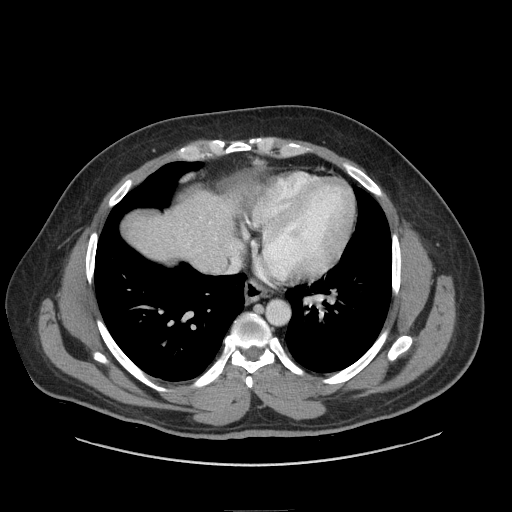
Contrast-enhanced abdominal CT (liver protocol), one axial slice; position 77 of 87 along the scan axis; 140 kVp; soft-tissue window (W 400 / L 40 HU); 2.5 mm slice thickness; 512 × 512 image matrix, field of view 440 × 440 mm. From the clinical record (not read from this slice): diagnosis: hepatocellular carcinoma (patient treated with transarterial chemoembolisation; whether this scan precedes or follows treatment is not stated here); TNM stage (as recorded): Stage-II; Child-Pugh class: A; tumour differentiation: moderately differentiated.
Outlined on this slice (semi-automatic segmentation, software-assisted and operator-edited):
- abdominal aorta: bounding box <267,301,289,325> (left, top, right, bottom; pixels)
- liver parenchyma outside the tumour (the mass and vessels are separate outlines, so this box may not span the whole liver): <124,192,236,264>